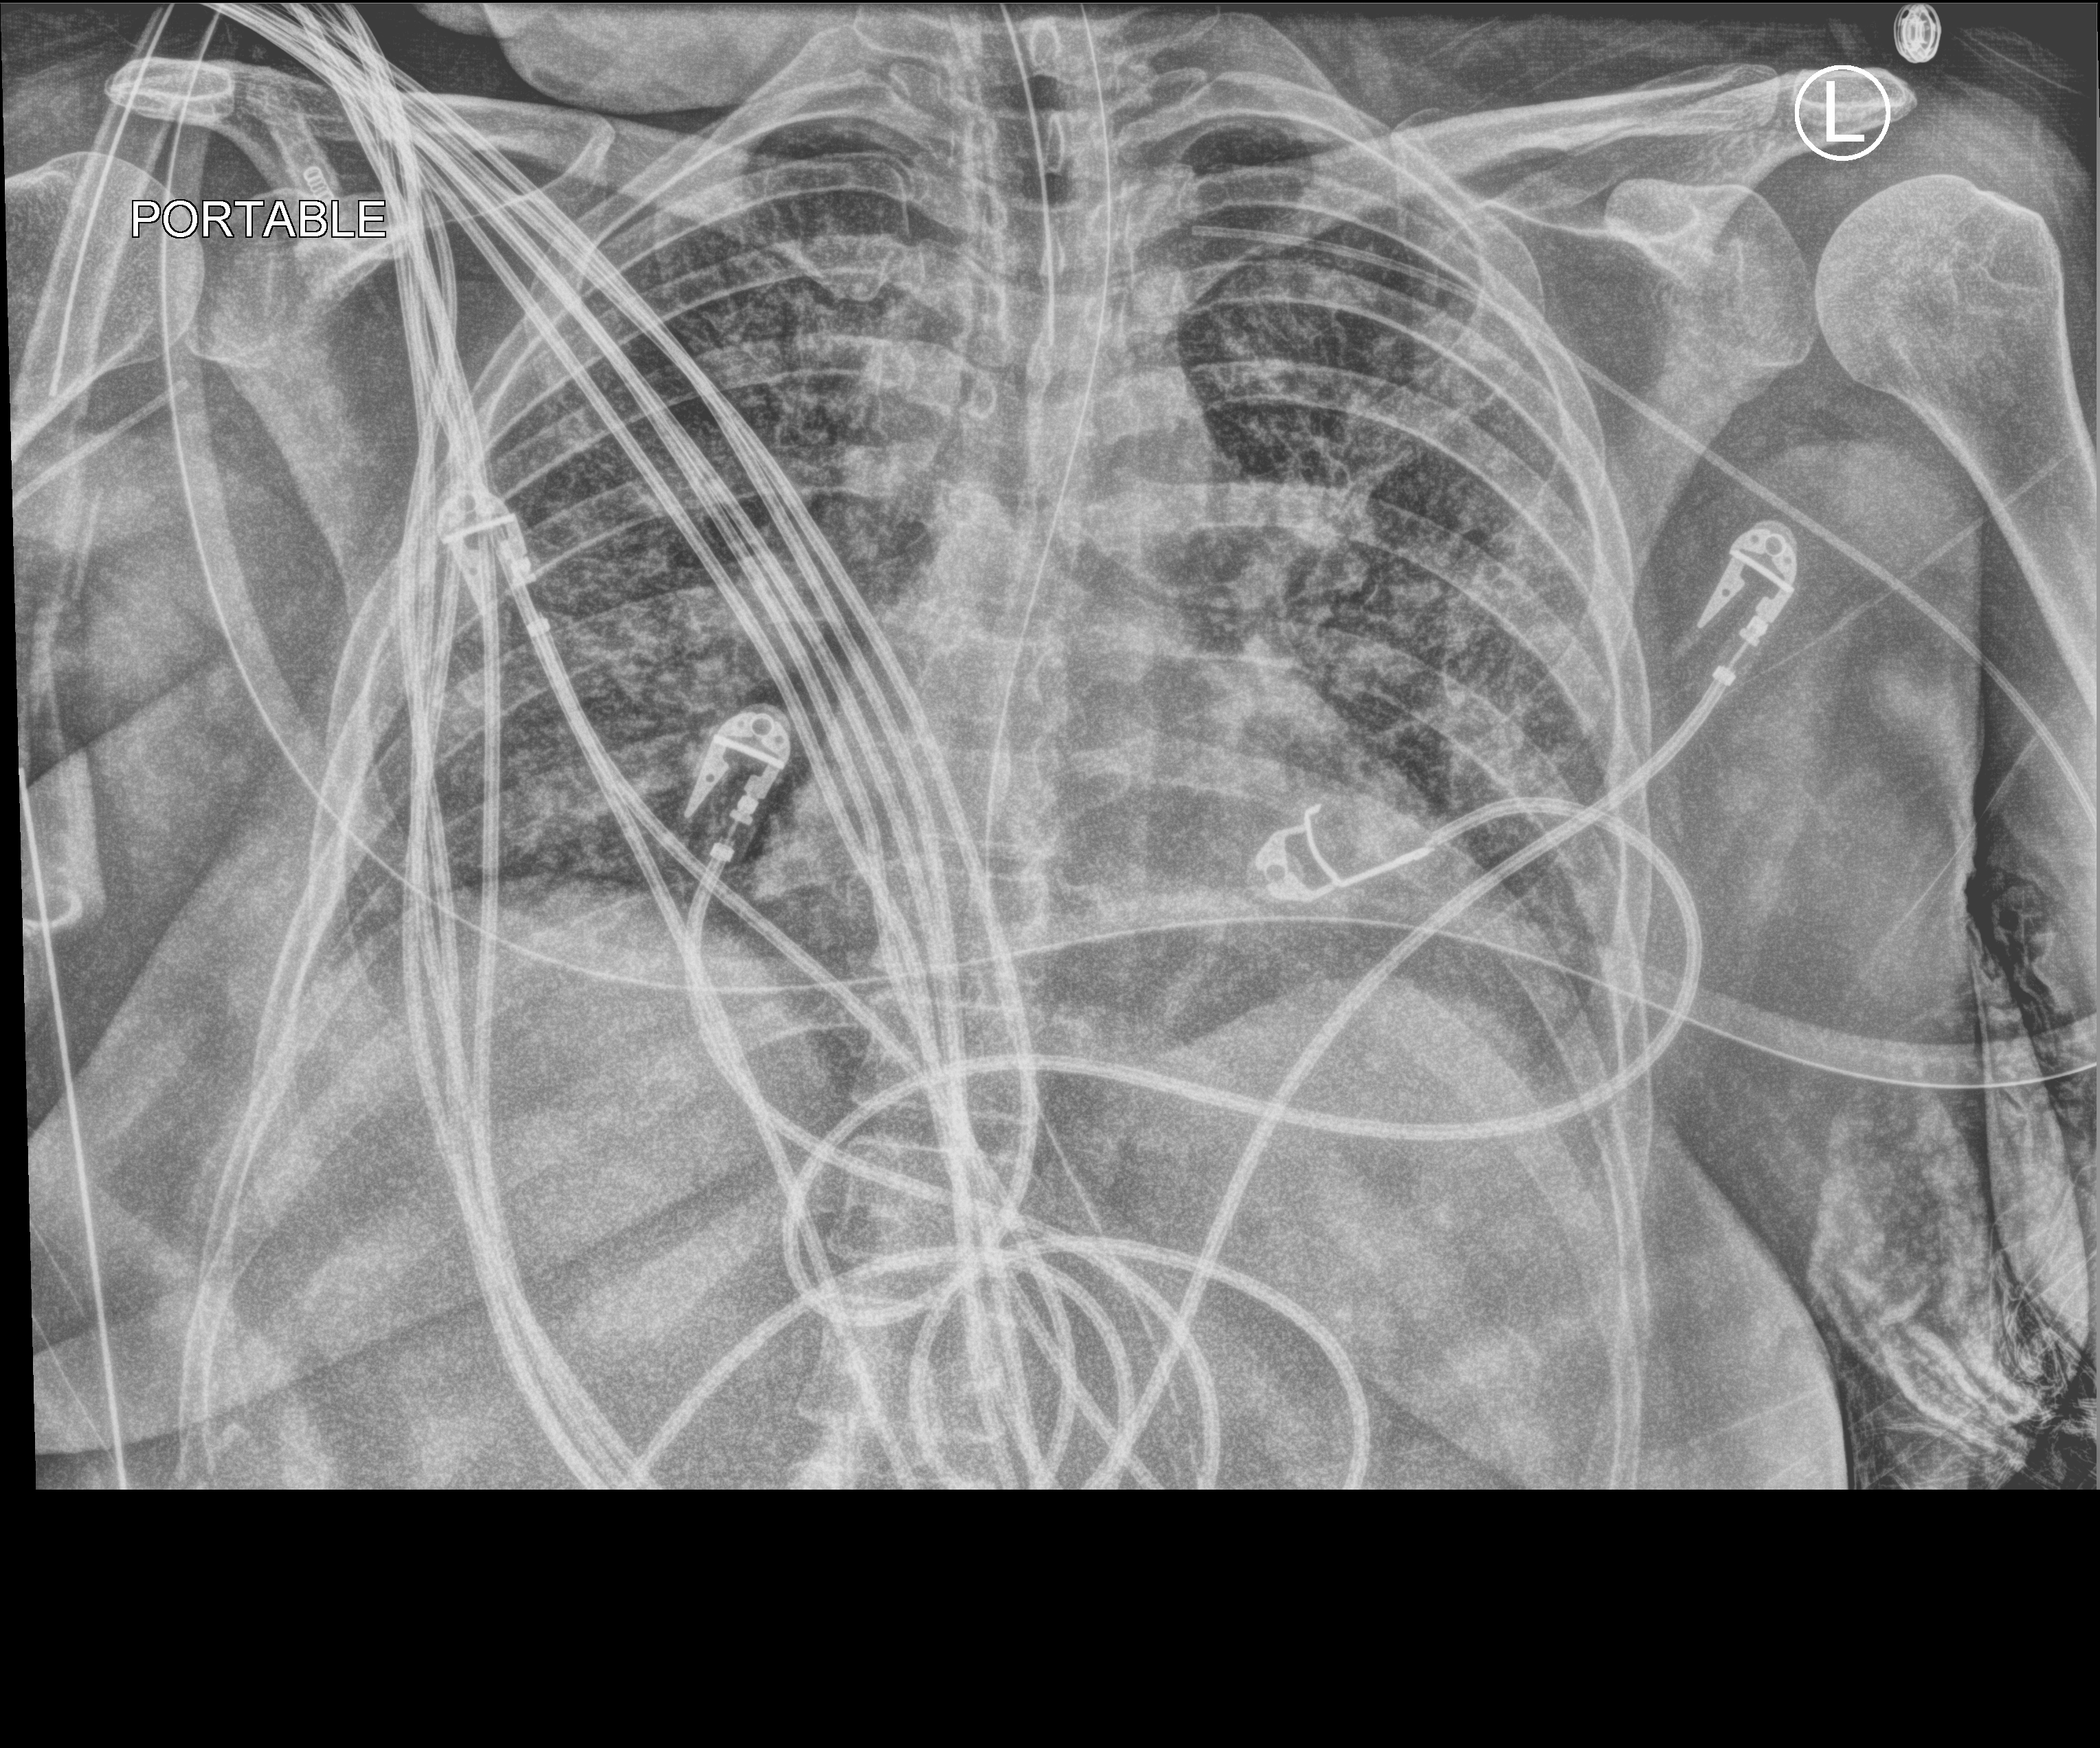
Portable chest radiograph. Female patient hospitalised with COVID-19, age 18–59 years.
Admission-level facts for this patient (not findings on this image; timing relative to this image not recorded): mechanically ventilated during this hospital stay: yes; smoking status (admission record): never; chronic kidney disease (admission record): no.